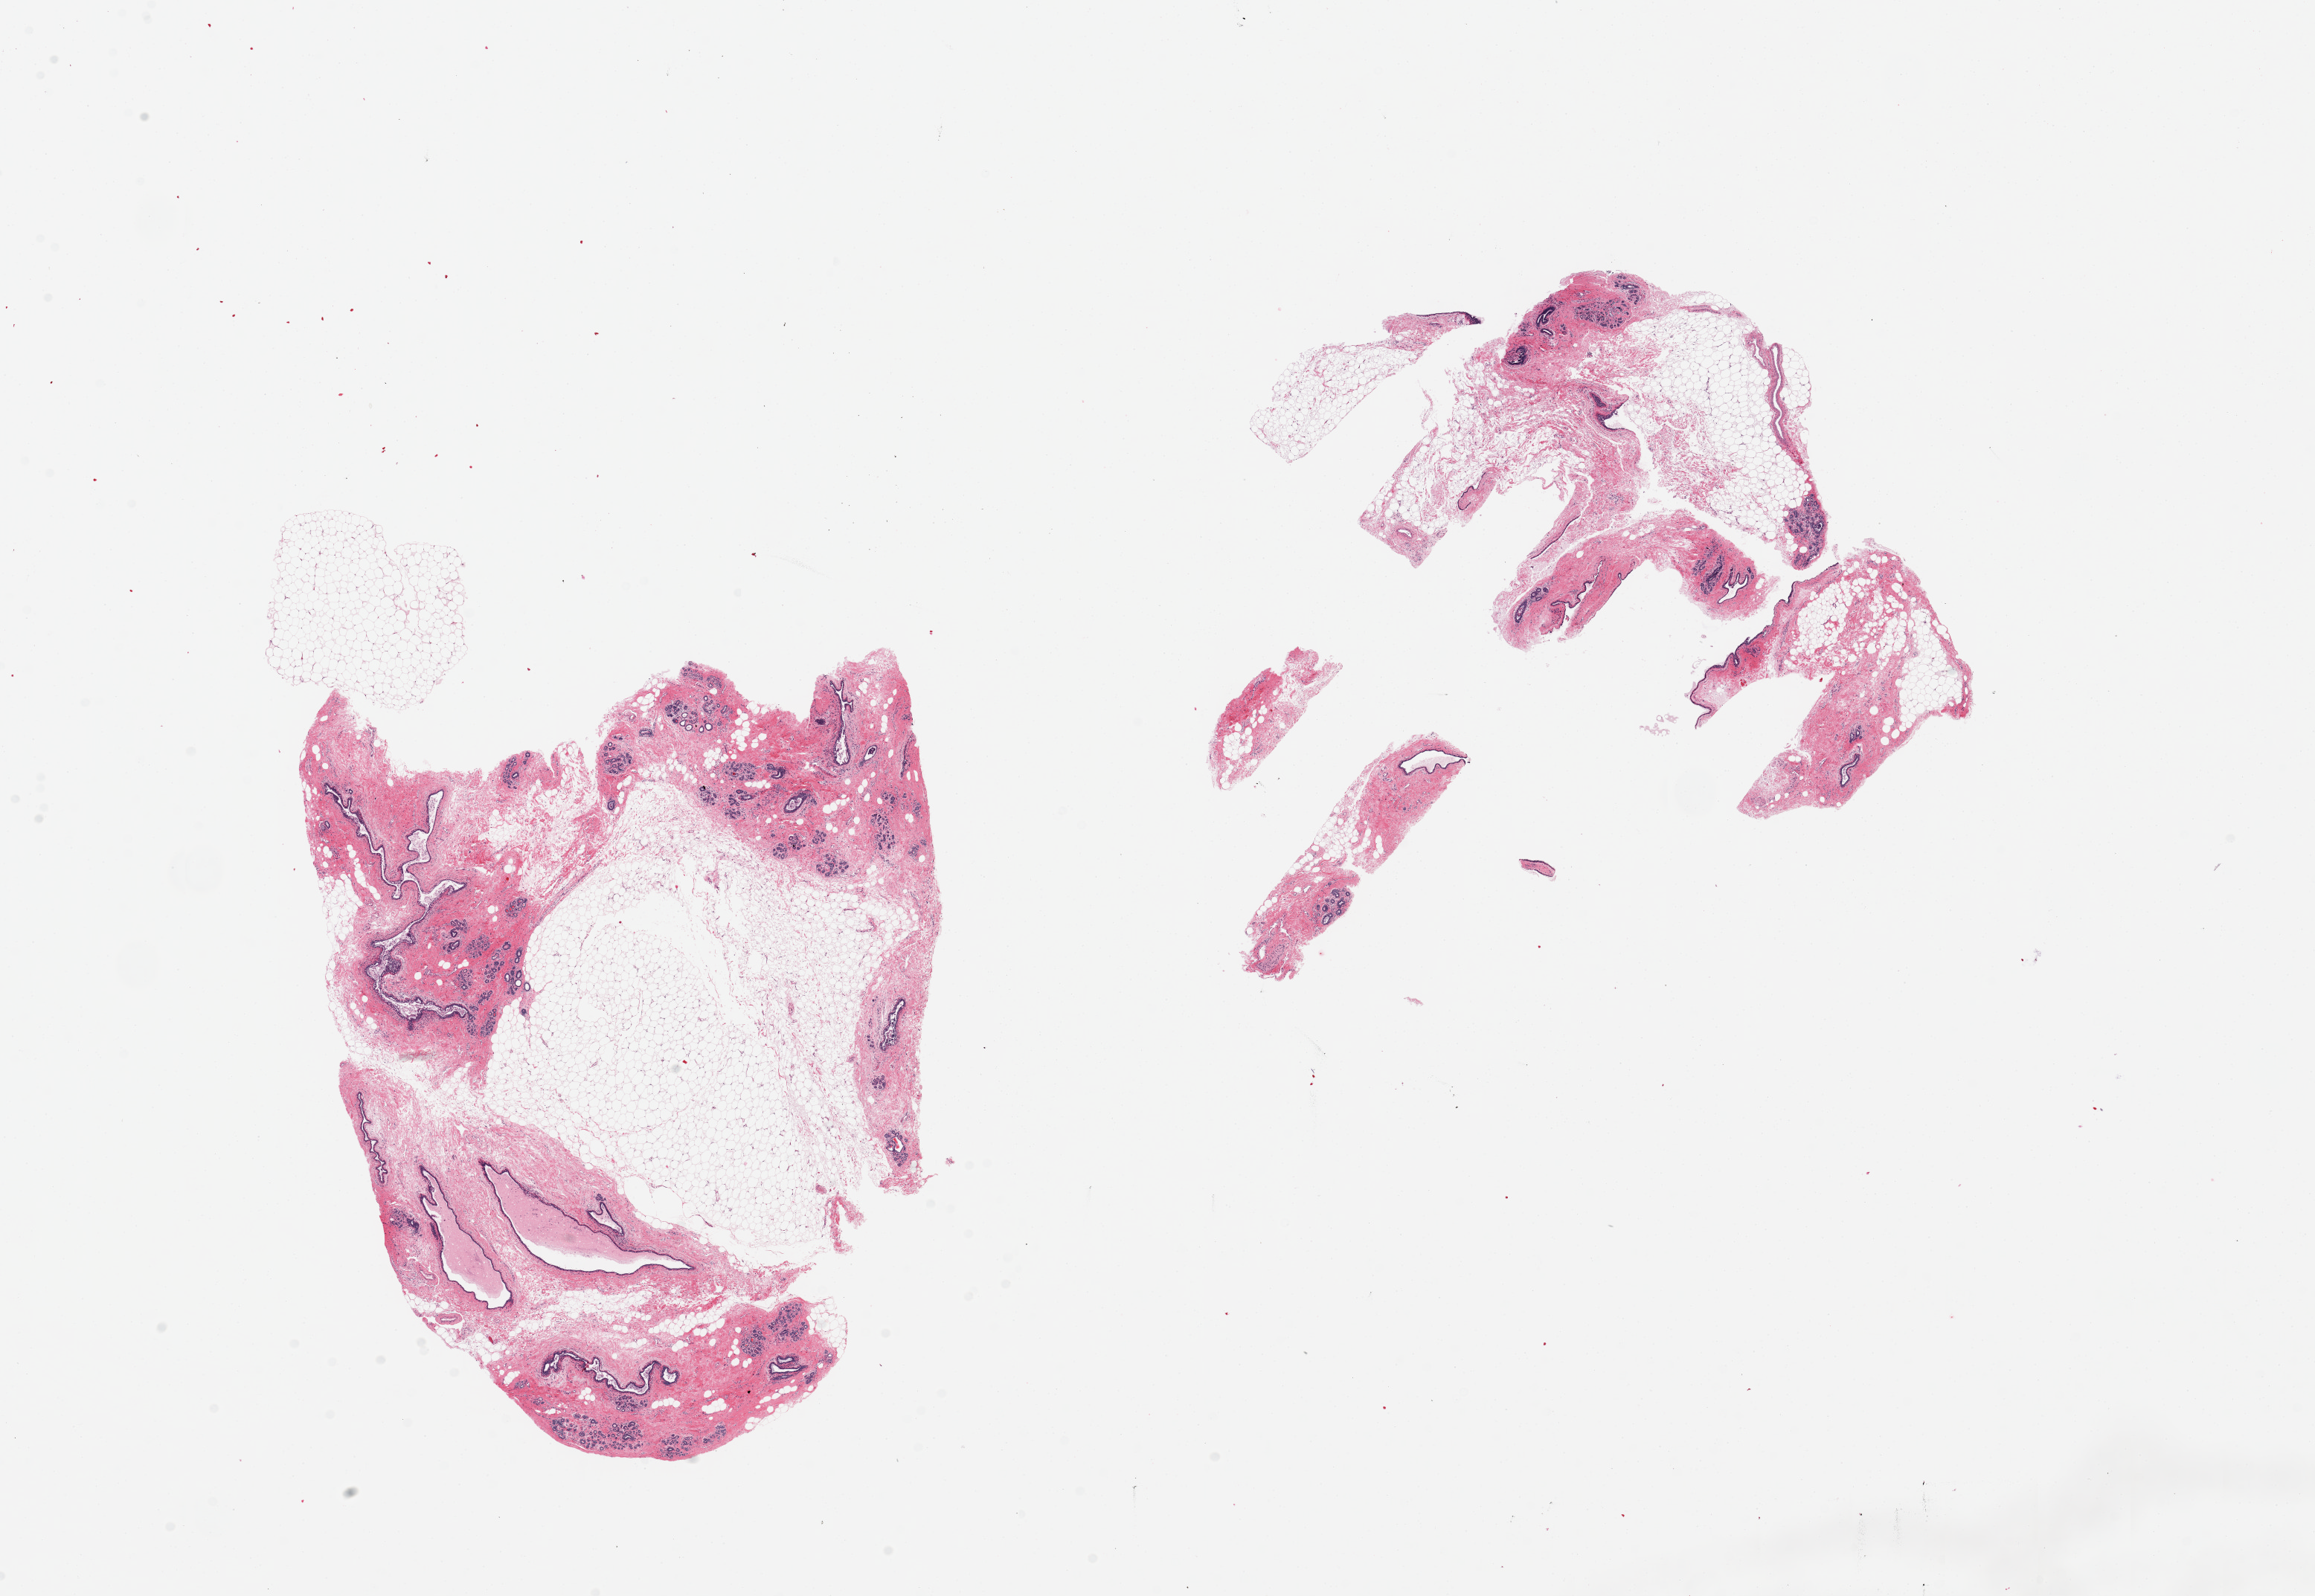
Whole-slide image, haematoxylin and eosin stain — a low-resolution overview of the entire scanned area, about 24.6 x 17.0 mm; PAXgene-fixed paraffin-embedded (PFPE) section; section of breast (target tissue); tissue donor sample.
Reviewer comment on this tissue sample: 2 pieces, 10.5x7 & 8.5x8mm; Ducts and lobules. 60% adipose.